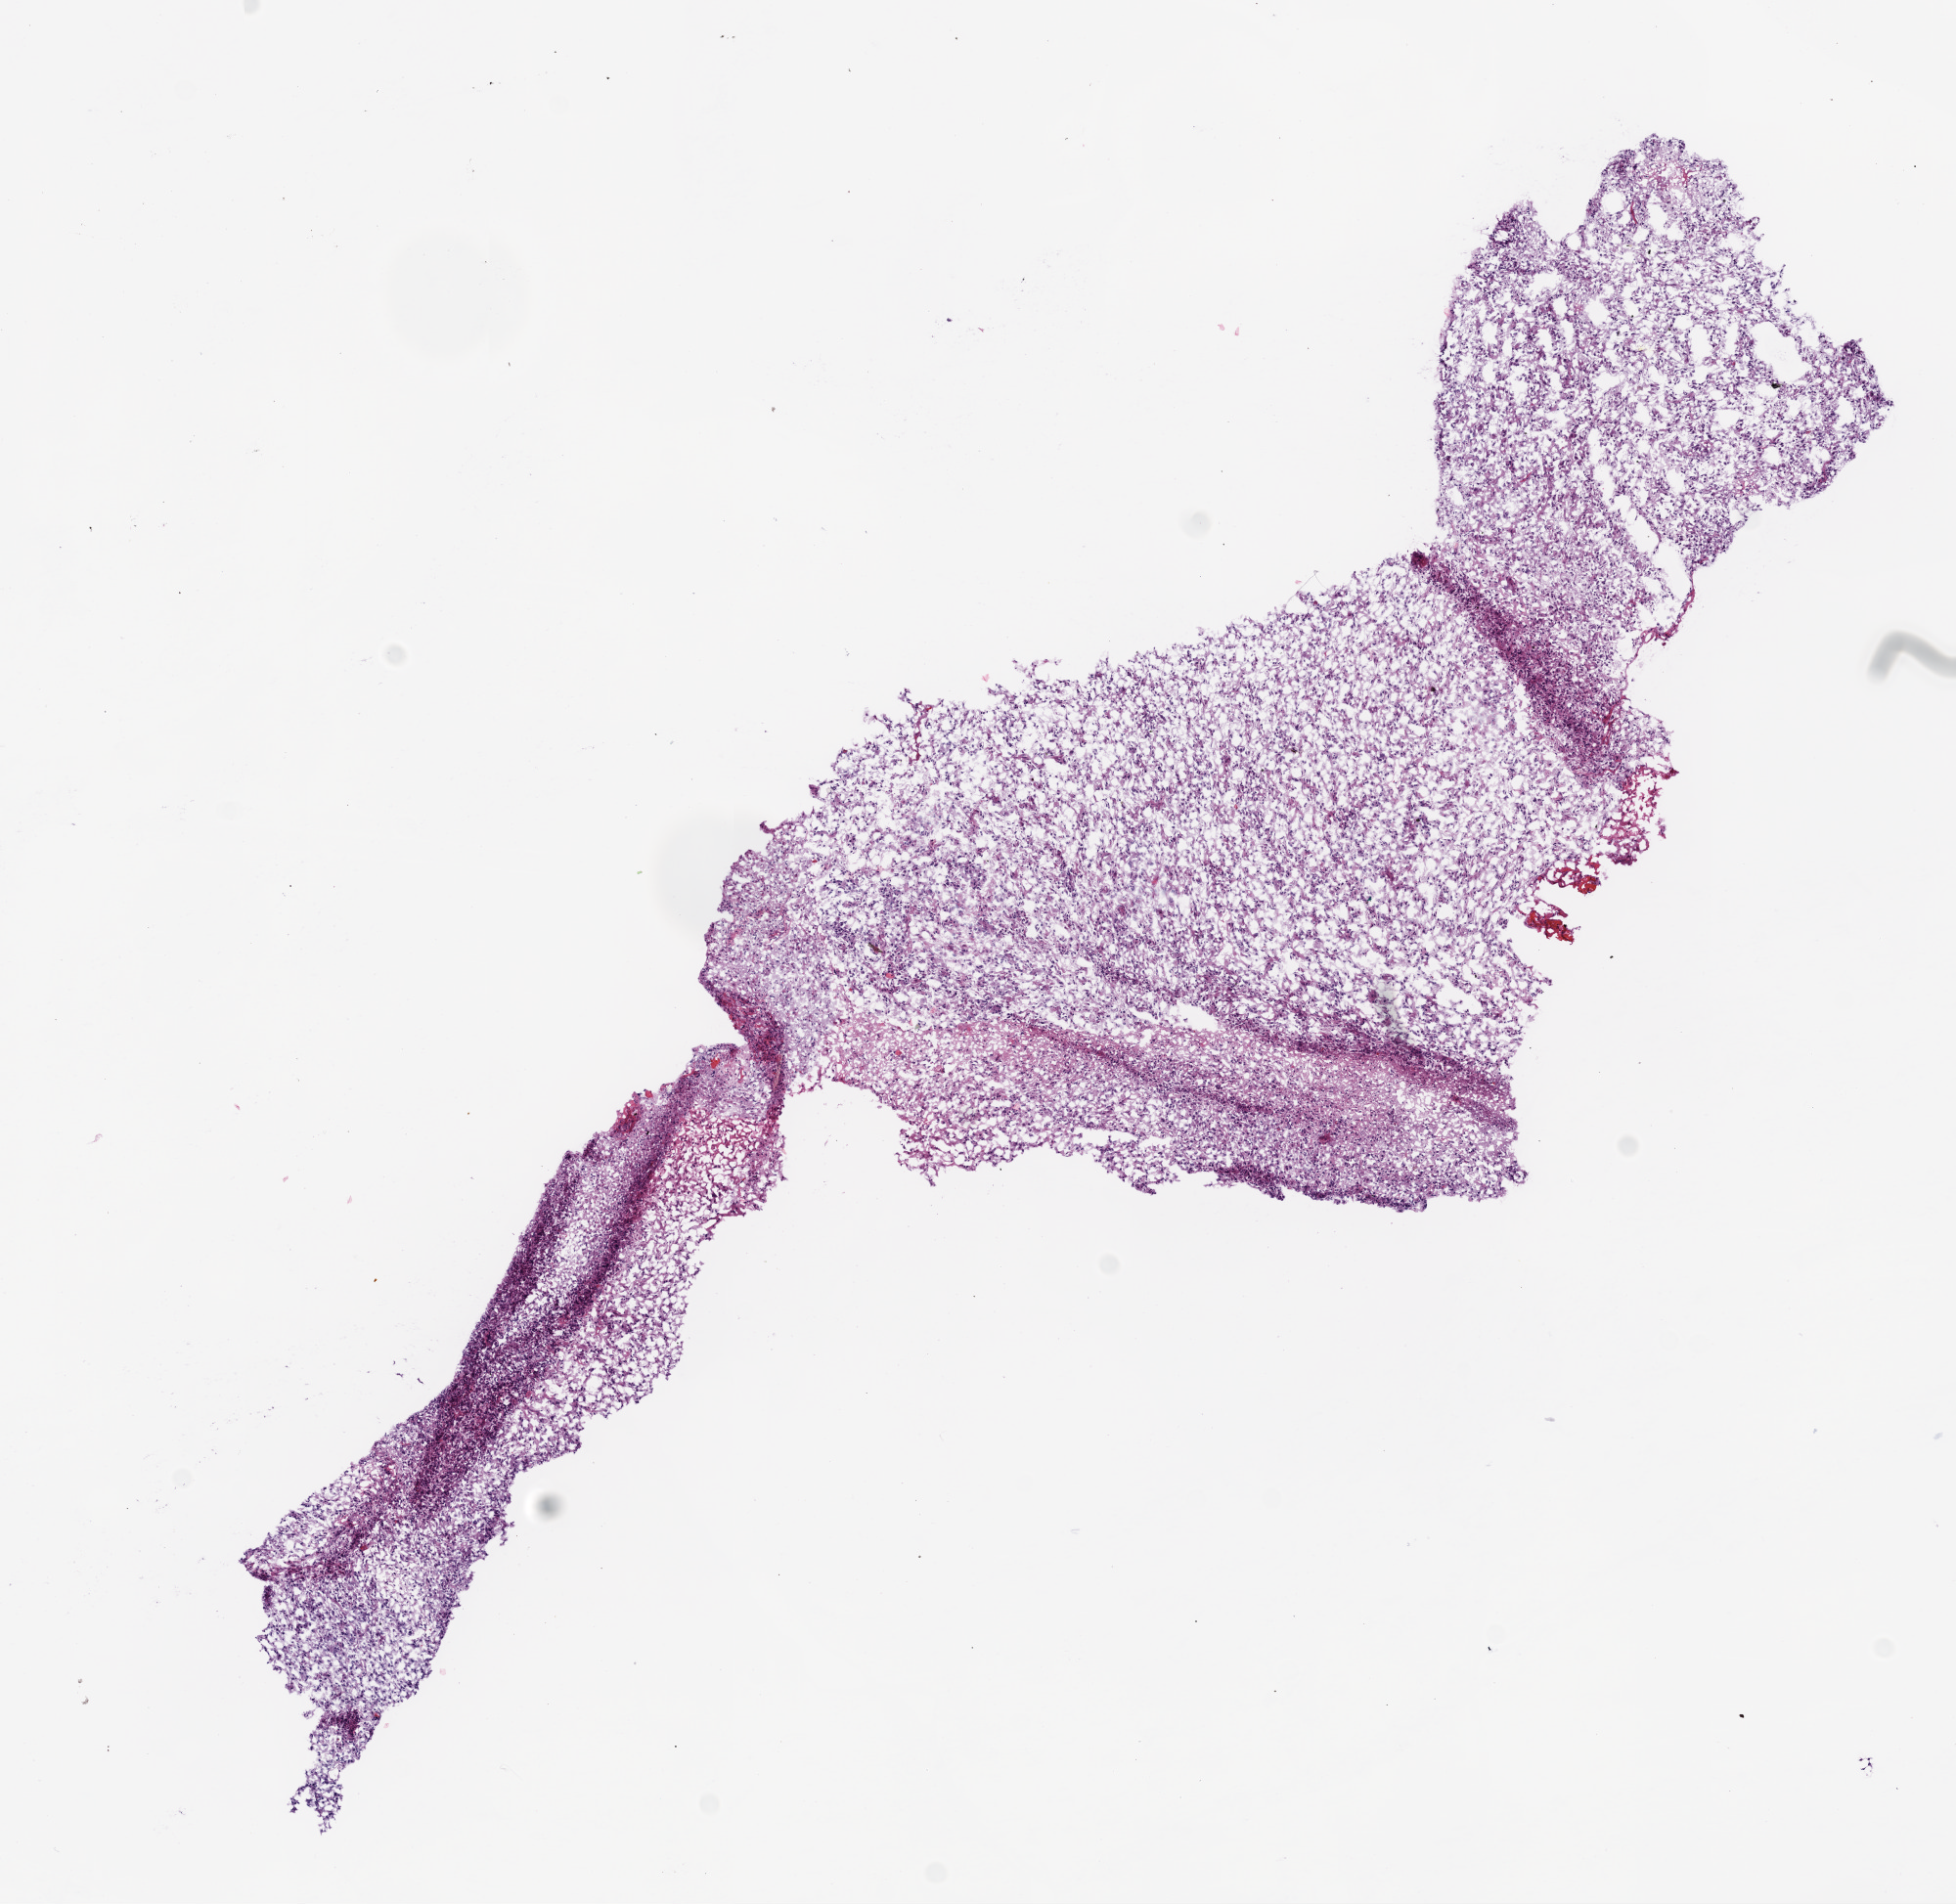
Whole-slide histology image, H&E-stained, whole scanned area (about 8.0 x 7.8 mm) shown as a low-resolution overview, frozen section, brain, primary tumour sample. Male patient; age at initial diagnosis 67 years. Composition of this section per pathologist review: tumour cells 95%, tumour nuclei 75%, normal cells 0%, stromal cells 0%, necrosis 5%.
Diagnosis: Glioblastoma.